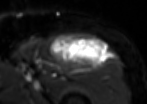
MRI of an extremity soft-tissue mass, one axial slice. Position 70 of 85 along the scan axis. T2-weighted fat-saturated. MR volume resampled by the dataset authors to the PET/CT grid (not the native acquisition matrix). 3.27 mm slice thickness. 147 × 104 image matrix, field of view 144 × 102 mm. Male patient. From the clinical record (not read from this slice): histological type: extraskeletal osteosarcoma; grade: high; site of the primary tumour: thigh.
Annotated regions visible in this slice (expert contour drawn on MRI and transferred to this co-registered scan by the dataset authors):
- gross tumour volume (mass): box from (x=49, y=35) to (x=107, y=68) px